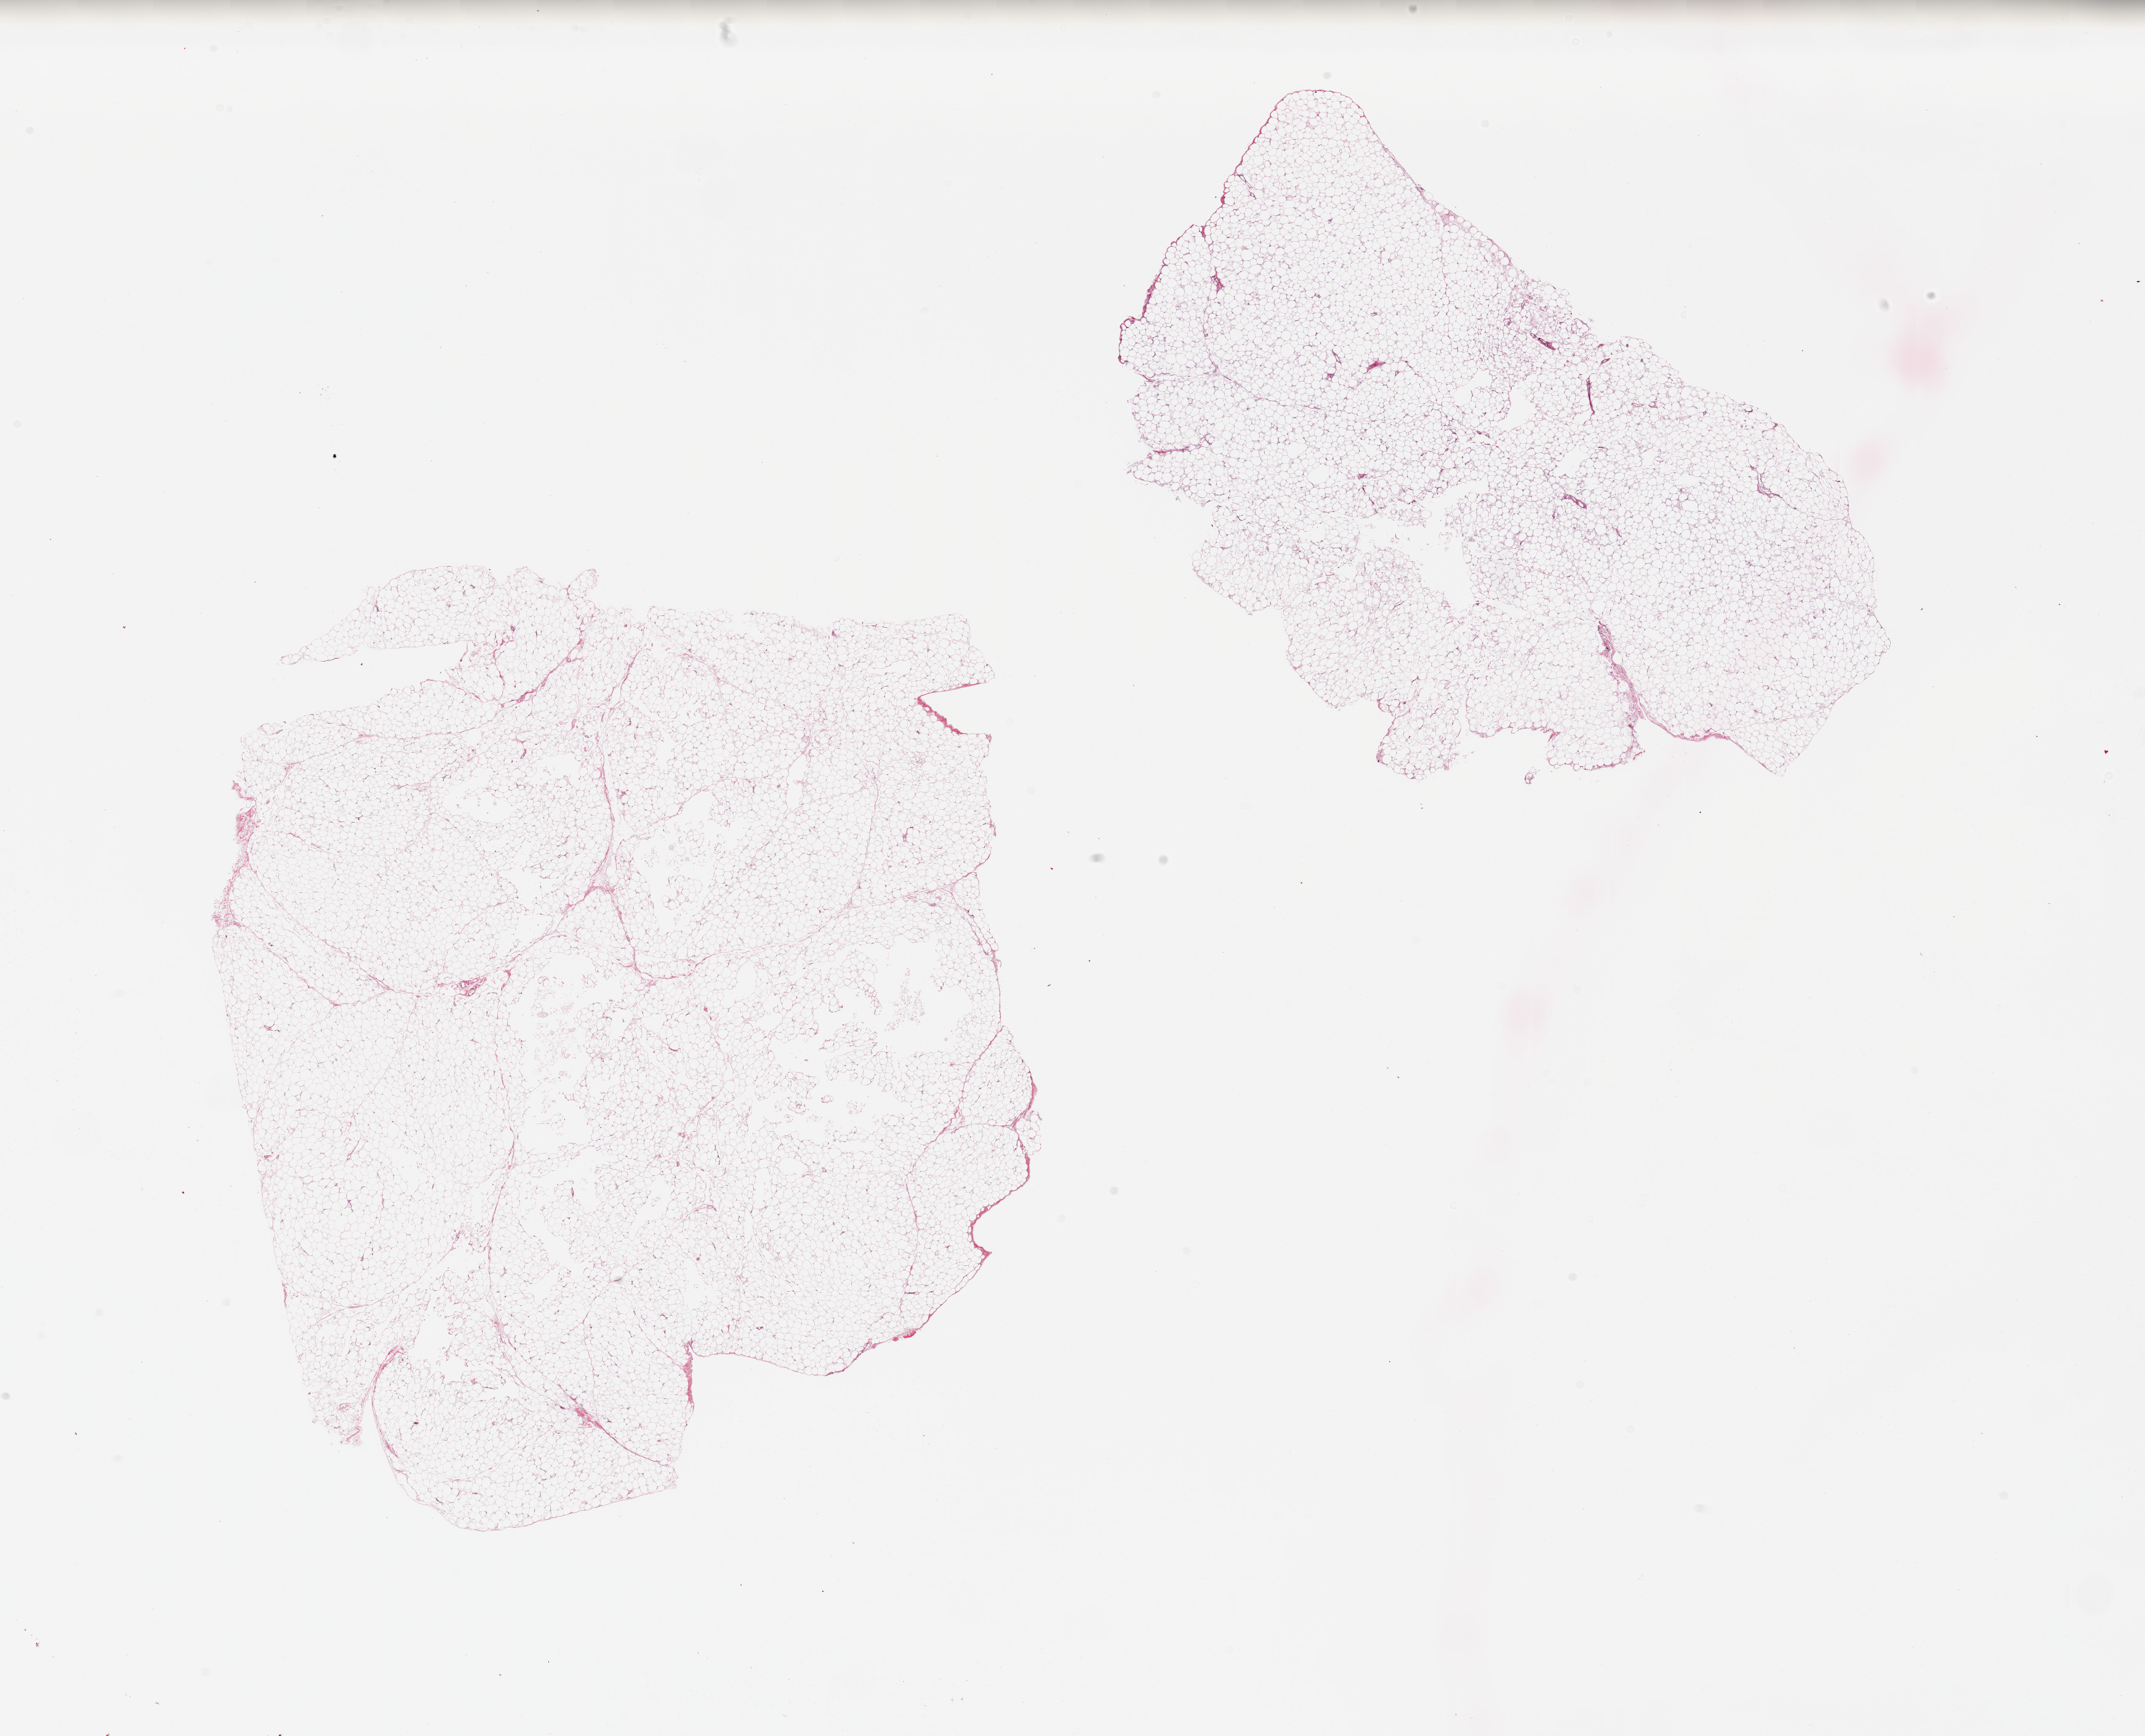
Digitized hematoxylin and eosin (H&E)-stained section — whole scanned area (about 27.6 x 22.3 mm) shown as a low-resolution overview. PAXgene-fixed, paraffin-embedded tissue. Target tissue: omentum. Tissue donor sample. Male donor.
• review note (as recorded): 2 pieces